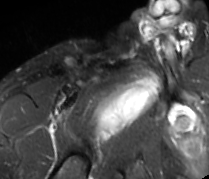
MRI of an extremity soft-tissue mass, one axial slice; position 73 of 89 along the scan axis; STIR; MR volume resampled by the dataset authors to the PET/CT grid (not the native acquisition matrix); 3.27 mm slice thickness; 209 × 179 image matrix. Male patient. From the clinical record (not read from this slice): histological type: undifferentiated - pleiomorphic; grade: high; site of the primary tumour: right thigh.
Outlined on this slice (expert contour drawn on MRI and transferred to this co-registered scan by the dataset authors):
- gross tumour volume including surrounding oedema: bounding box [x1, y1, x2, y2] px = [94, 71, 161, 143]
- gross tumour volume (mass): [94, 76, 157, 136]